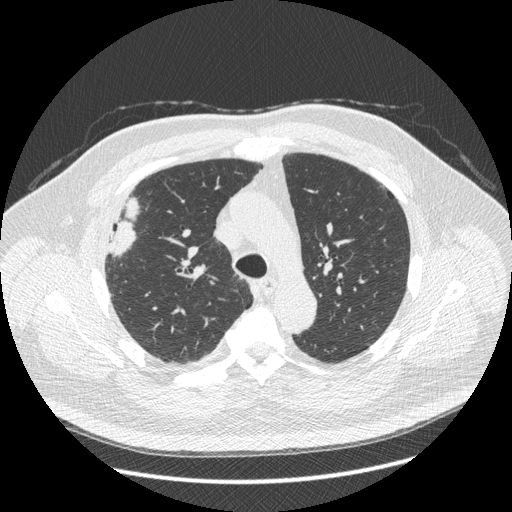
Low-dose screening chest CT, one axial slice; 120 kVp; lung window (W 1500 / L -600 HU); 512 × 512 image matrix, field of view 400 × 400 mm.
Structures marked on this image (manually delineated by an expert):
- lesion 1 (tumor, upper lobe of right lung): bounding box <108,198,138,255> (left, top, right, bottom; pixels)